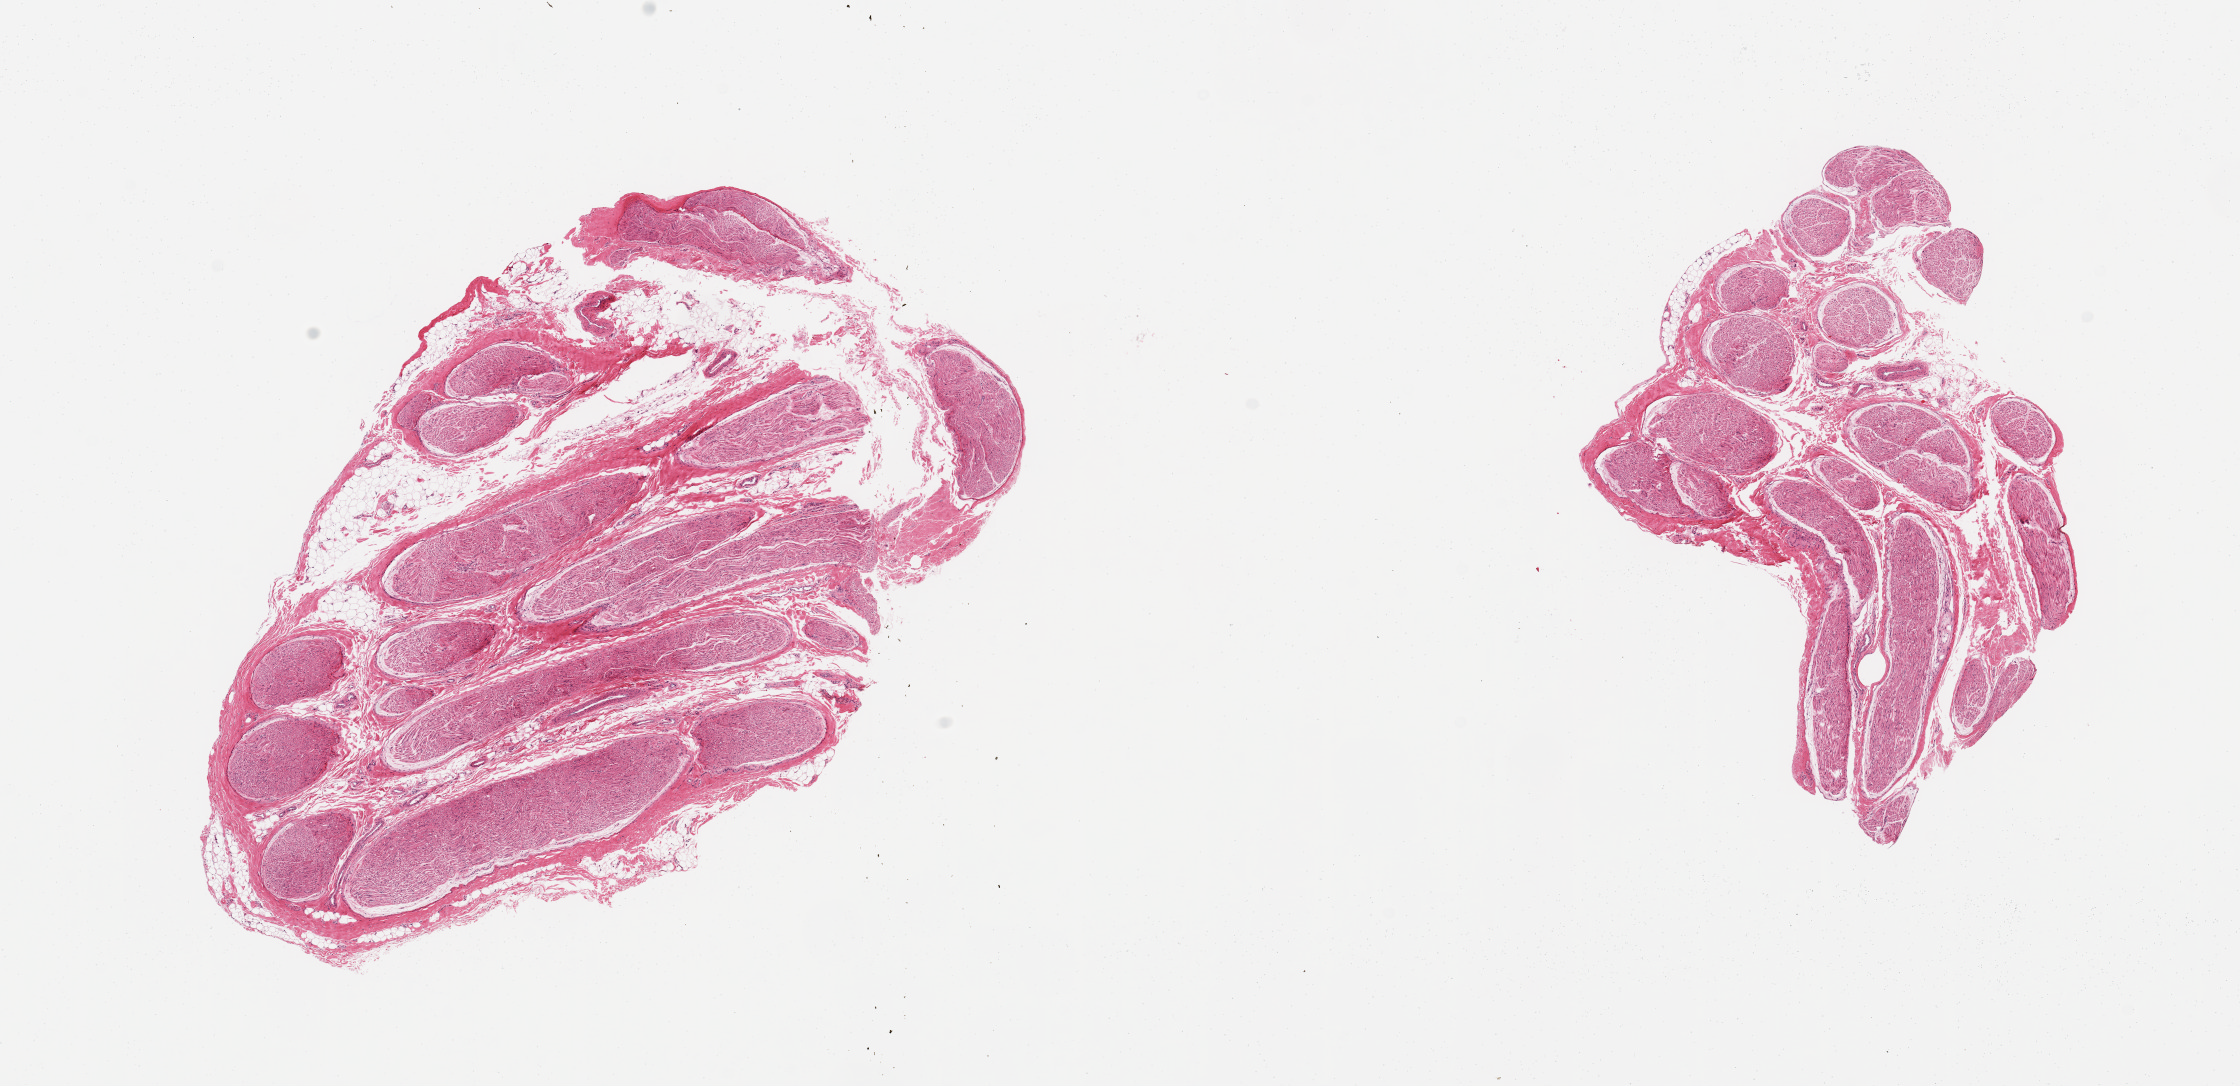
Digitized haematoxylin and eosin-stained section, shown as a low-resolution overview of the whole scanned area (about 17.7 x 8.6 mm, acquisition: 20x scan), PAXgene-fixed paraffin-embedded (PFPE) section, sampled site (target tissue): tibial nerve, tissue donor sample.
Reviewer comment on this tissue sample: 2 pieces; 10% internal fat.